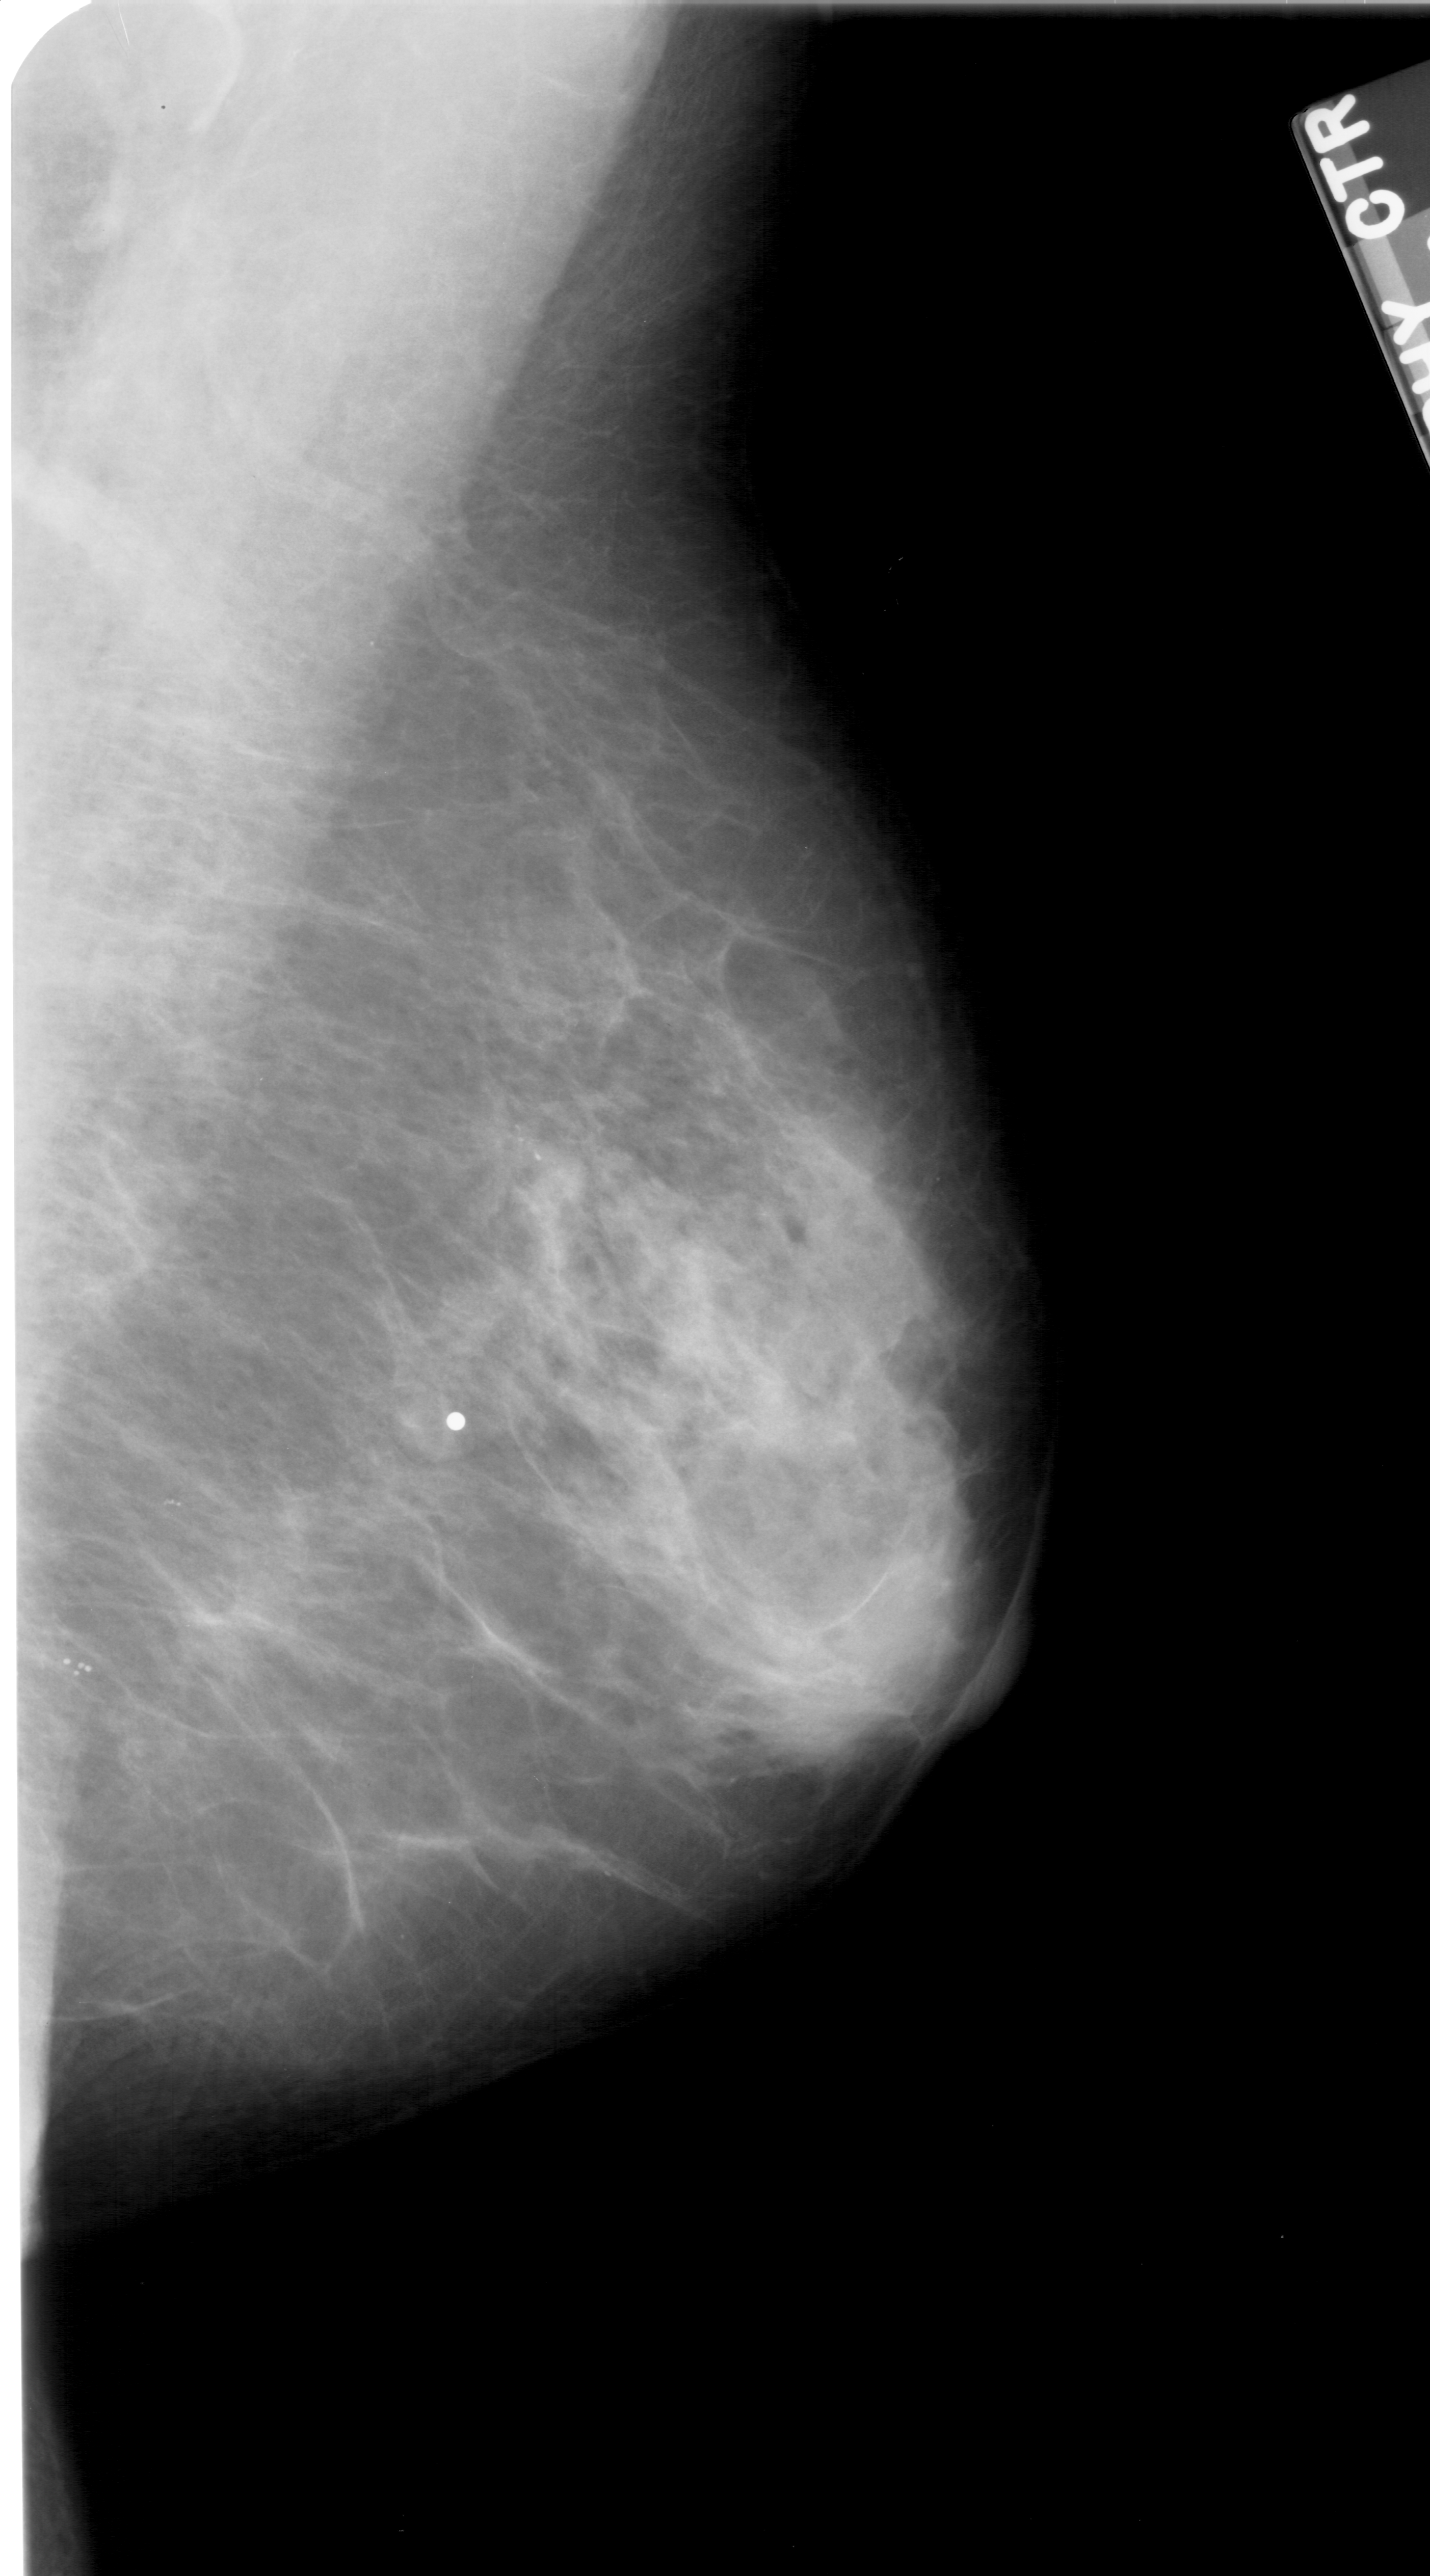
Digitized screen-film mammogram. Right breast. MLO view. Breast composition: scattered fibroglandular densities (BI-RADS density category 2 of 4). 1430 × 2576 image matrix.
Expert-marked regions of interest on this image (one box per marked abnormality):
- calcifications, morphology pleomorphic, distribution clustered; BI-RADS assessment category 4; subtlety rating 2 on a 1 (subtle) to 5 (obvious) scale; pathology result (as recorded, not read from the image): malignant: box from (x=491, y=1114) to (x=578, y=1189) px